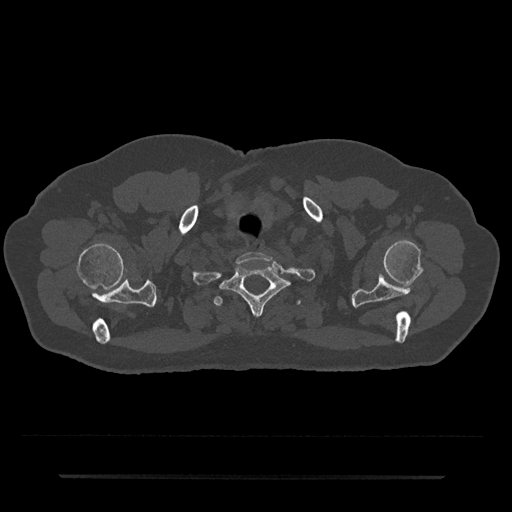
CT including the spine, one axial slice. Slice 640 of 797 in the series (ordered by position). Bone window (W 1800 / L 400 HU). 512 × 512 image matrix, field of view 437 × 437 mm. Patient: male, 69 years. From the clinical record (not read from this slice): primary cancer: prostate.
Structures marked on this image (semi-automatically segmented with operator editing):
- T1 vertebra: bounding box (x1, y1, x2, y2) in pixels: (219, 263, 292, 316)
- T2 vertebra: (214, 296, 300, 306)